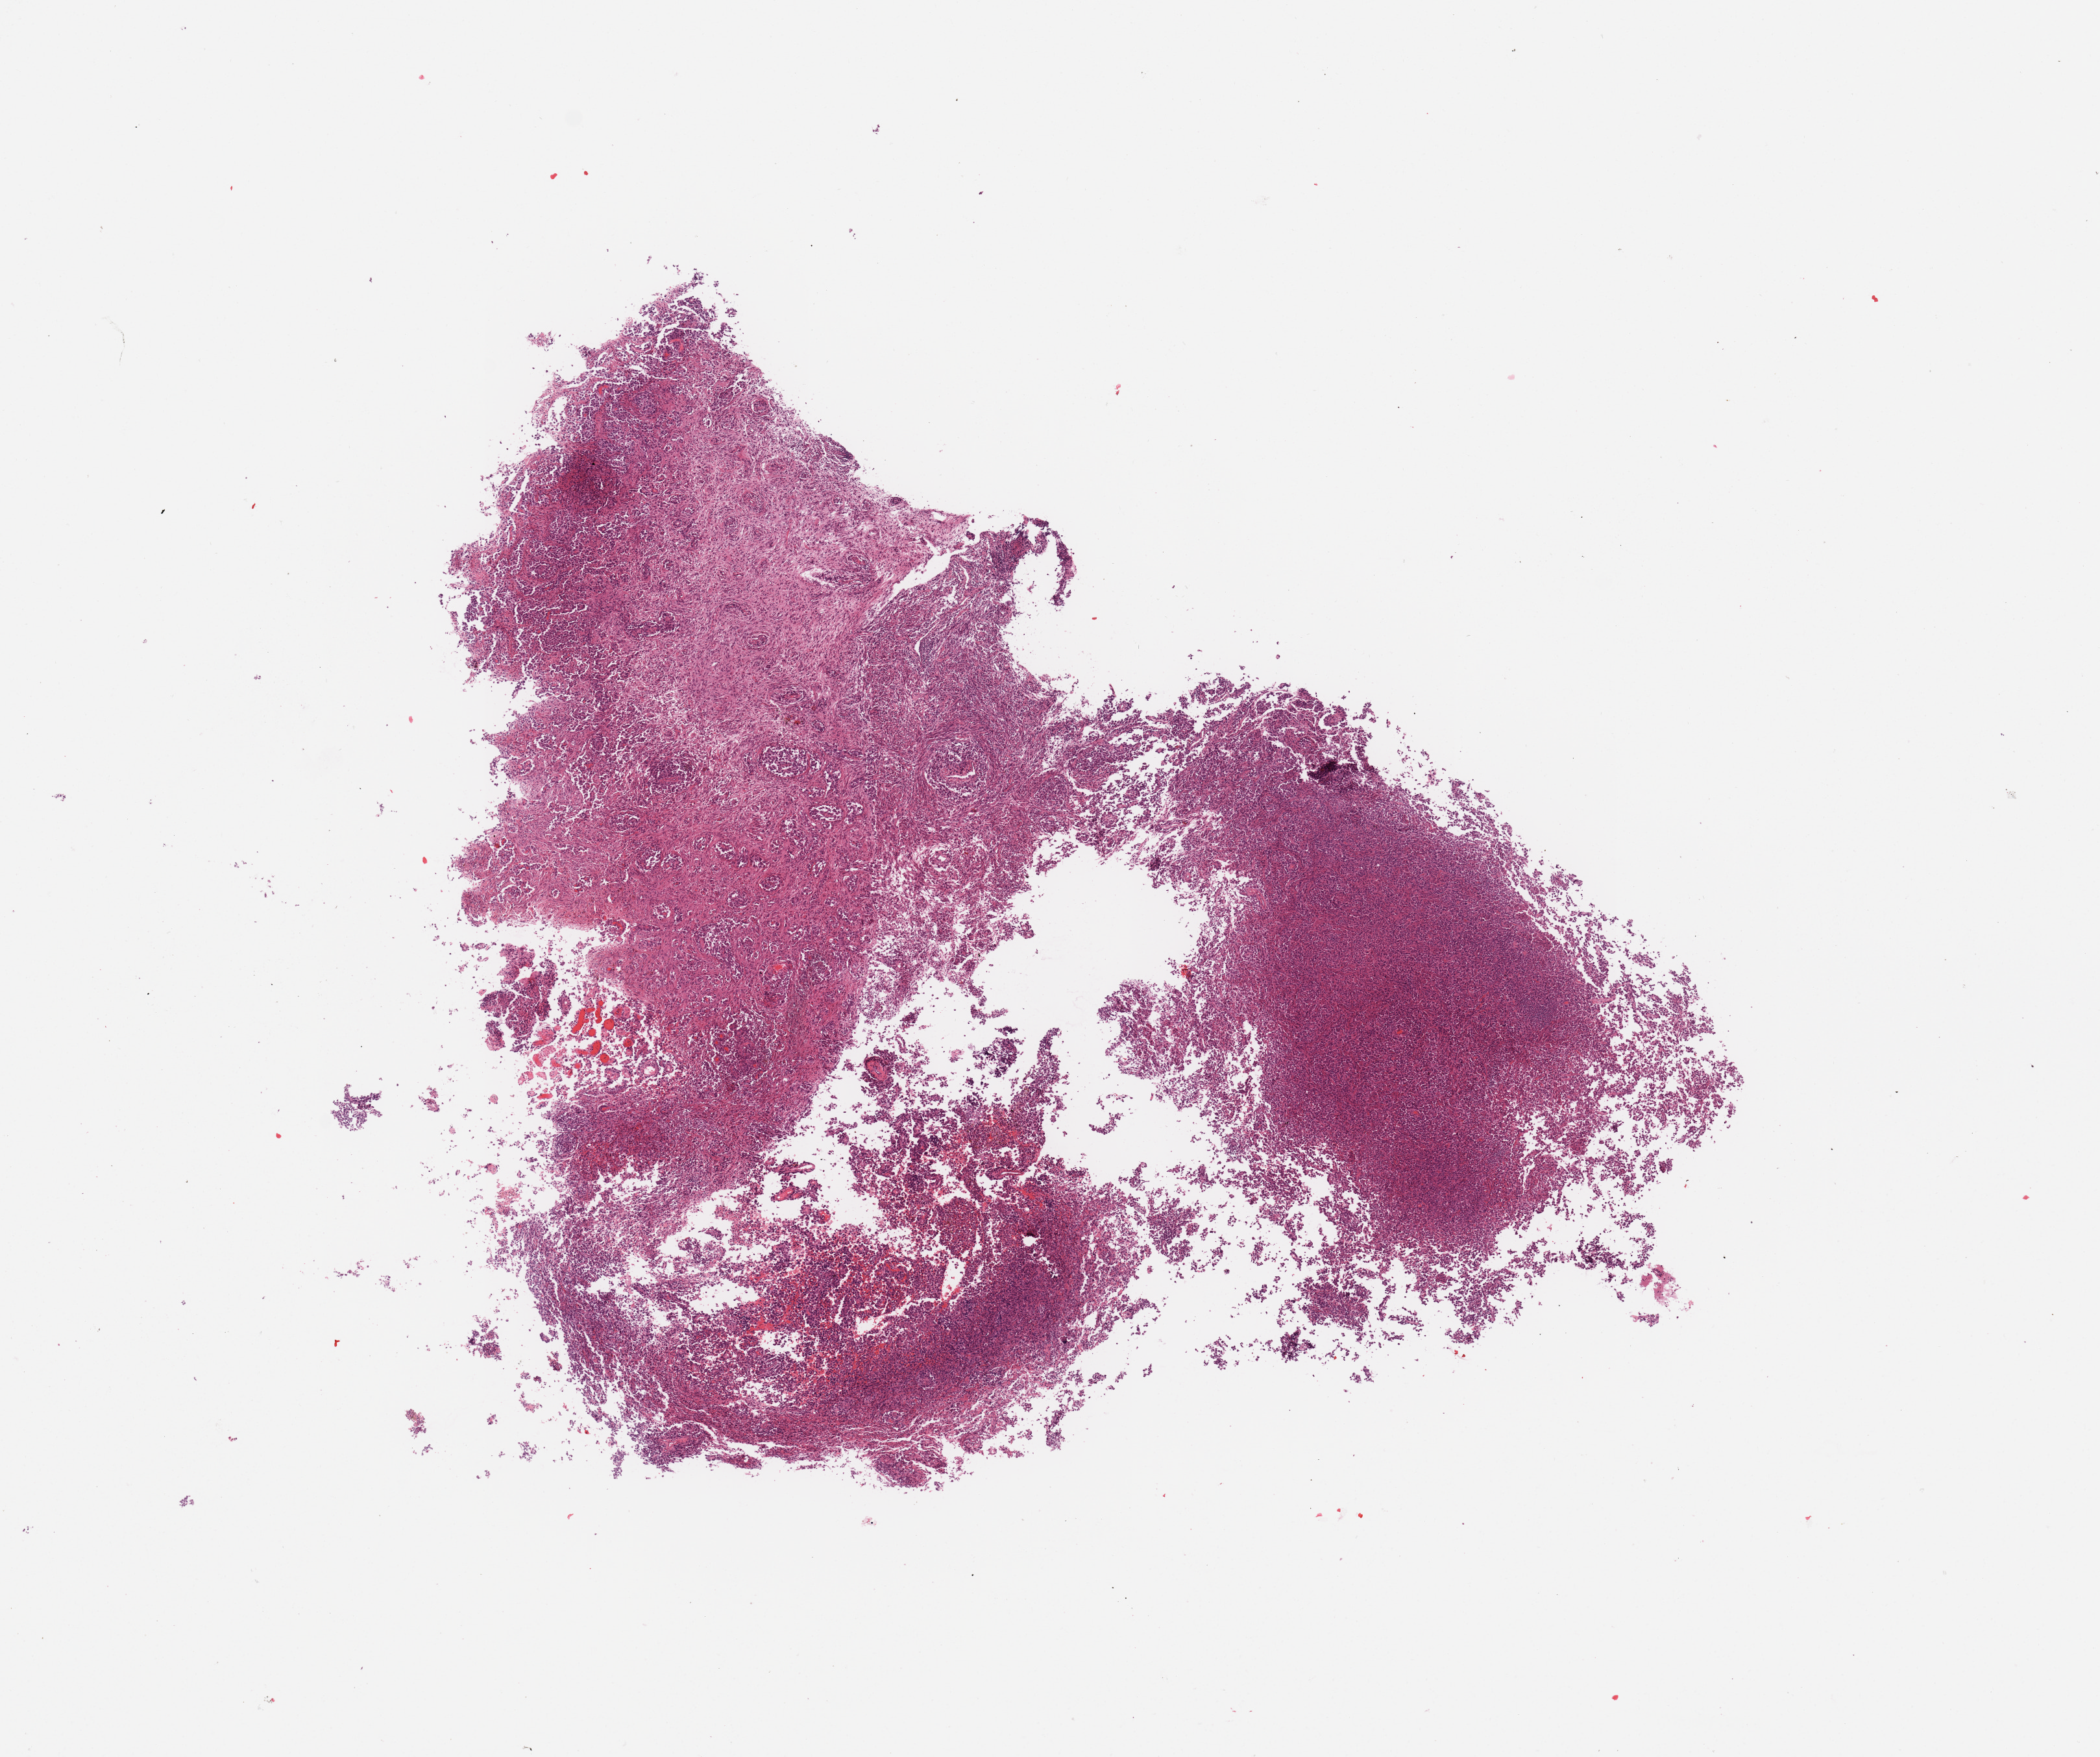
Digitized H&E tissue section (whole slide) — shown as a low-resolution overview of the whole scanned area (about 12.8 x 10.7 mm). Tumour tissue sample, sampled site: occipital cortex. Patient: female, age 31 years. Pathologist review of this section (percent, as recorded): tumour nuclei 80%, necrosis 5%.
Primary tumour site (as recorded): occipital lobe. Histologic diagnosis: Glioblastoma.